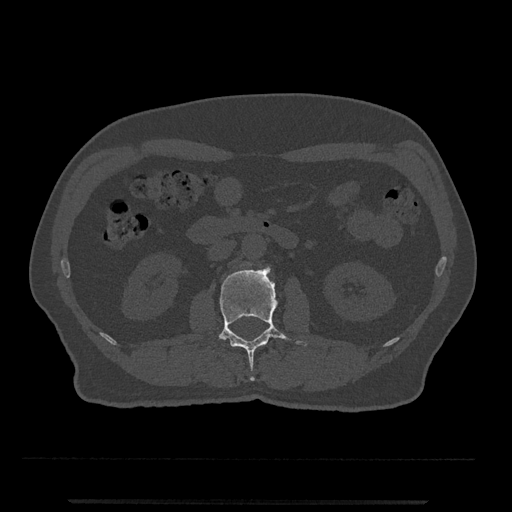
CT including the spine, one axial slice; slice 263 of 797 in the series (ordered by position); reconstruction kernel Br40s/3; 120 kVp; bone window (W 1800 / L 400 HU); 512 × 512 image matrix, field of view 419 × 419 mm. Male patient, age 63 years. Case-level facts recorded for this patient, not image findings: primary cancer: prostate.
Annotated regions visible in this slice (semi-automatic segmentation, software-assisted and operator-edited):
- L2 vertebra: box from (x=218, y=263) to (x=307, y=382) px